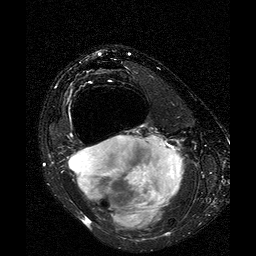
MRI of an extremity soft-tissue mass, one axial slice. Slice 19 of 25 in the series (ordered by position). T2-weighted fat-saturated. 256 × 256 image matrix, field of view 160 × 160 mm. Female patient. Case-level facts recorded for this patient, not image findings: histological type: liposarcoma; site of the primary tumour: right thigh.
Outlined on this slice (manually delineated by an expert):
- gross tumour volume (mass): bounding box <68,135,184,231> (left, top, right, bottom; pixels)